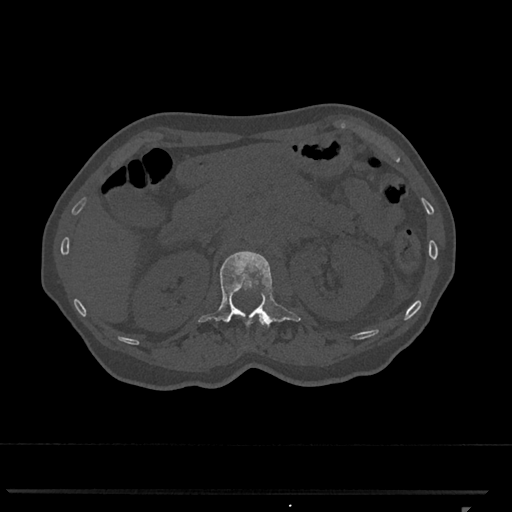
CT including the spine, one axial slice; slice 409 of 793 in the series (ordered by position); bone window (W 1800 / L 400 HU); 0.5 mm slice thickness; 512 × 512 image matrix, field of view 380 × 380 mm. Female patient, age 62 years. From the clinical record (not read from this slice): primary cancer: renal.
Structures marked on this image (semi-automatically segmented with operator editing):
- L1 vertebra: bounding box (x1, y1, x2, y2) in pixels: (198, 251, 301, 327)
- T12 vertebra: (259, 316, 265, 325)